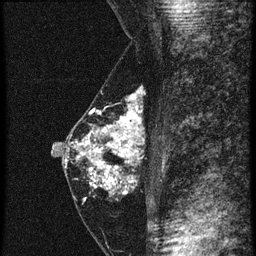
Breast MRI (dynamic contrast-enhanced), one sagittal slice. Position 25 of 60 along the scan axis. 4 images stored at this slice position (order not interpretable as contrast timing). 1.5 T. TE 4.2 ms, TR 20.4 ms. 1.5 mm slice thickness. 256 × 256 image matrix, field of view 180 × 180 mm. Female patient, age 46 years. Case-level facts recorded for this patient, not image findings: setting: breast cancer imaged before/during neoadjuvant chemotherapy; receptor status: triple-negative.
Structures marked on this image (semi-automatically segmented with operator editing):
- analysis volume of interest (the breast-tissue region the enhancement analysis was run in; not a lesion): bounding box <67,84,147,201> (left, top, right, bottom; pixels)
- tumour enhancement mask (voxels above the 90 % enhancement threshold inside the analysis volume of interest): <67,108,142,201>